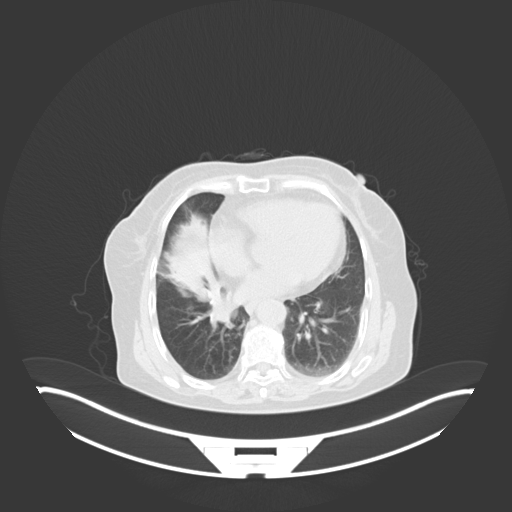
Chest CT, one axial slice; slice 18 of 76 in the series (ordered by position); reconstruction kernel B30f; 120 kVp; lung window (W 1500 / L -600 HU); 3 mm slice thickness; 512 × 512 image matrix, field of view 500 × 500 mm. Female patient, age 75 years. Case-level facts recorded for this patient, not image findings: clinical TNM (as recorded): T1b N0 M1a; histopathological grade: G1.
Structures marked on this image (rectangle marked by the reading radiologist):
- lung tumour (recorded histology: squamous cell carcinoma): box from (x=207, y=294) to (x=240, y=327) px